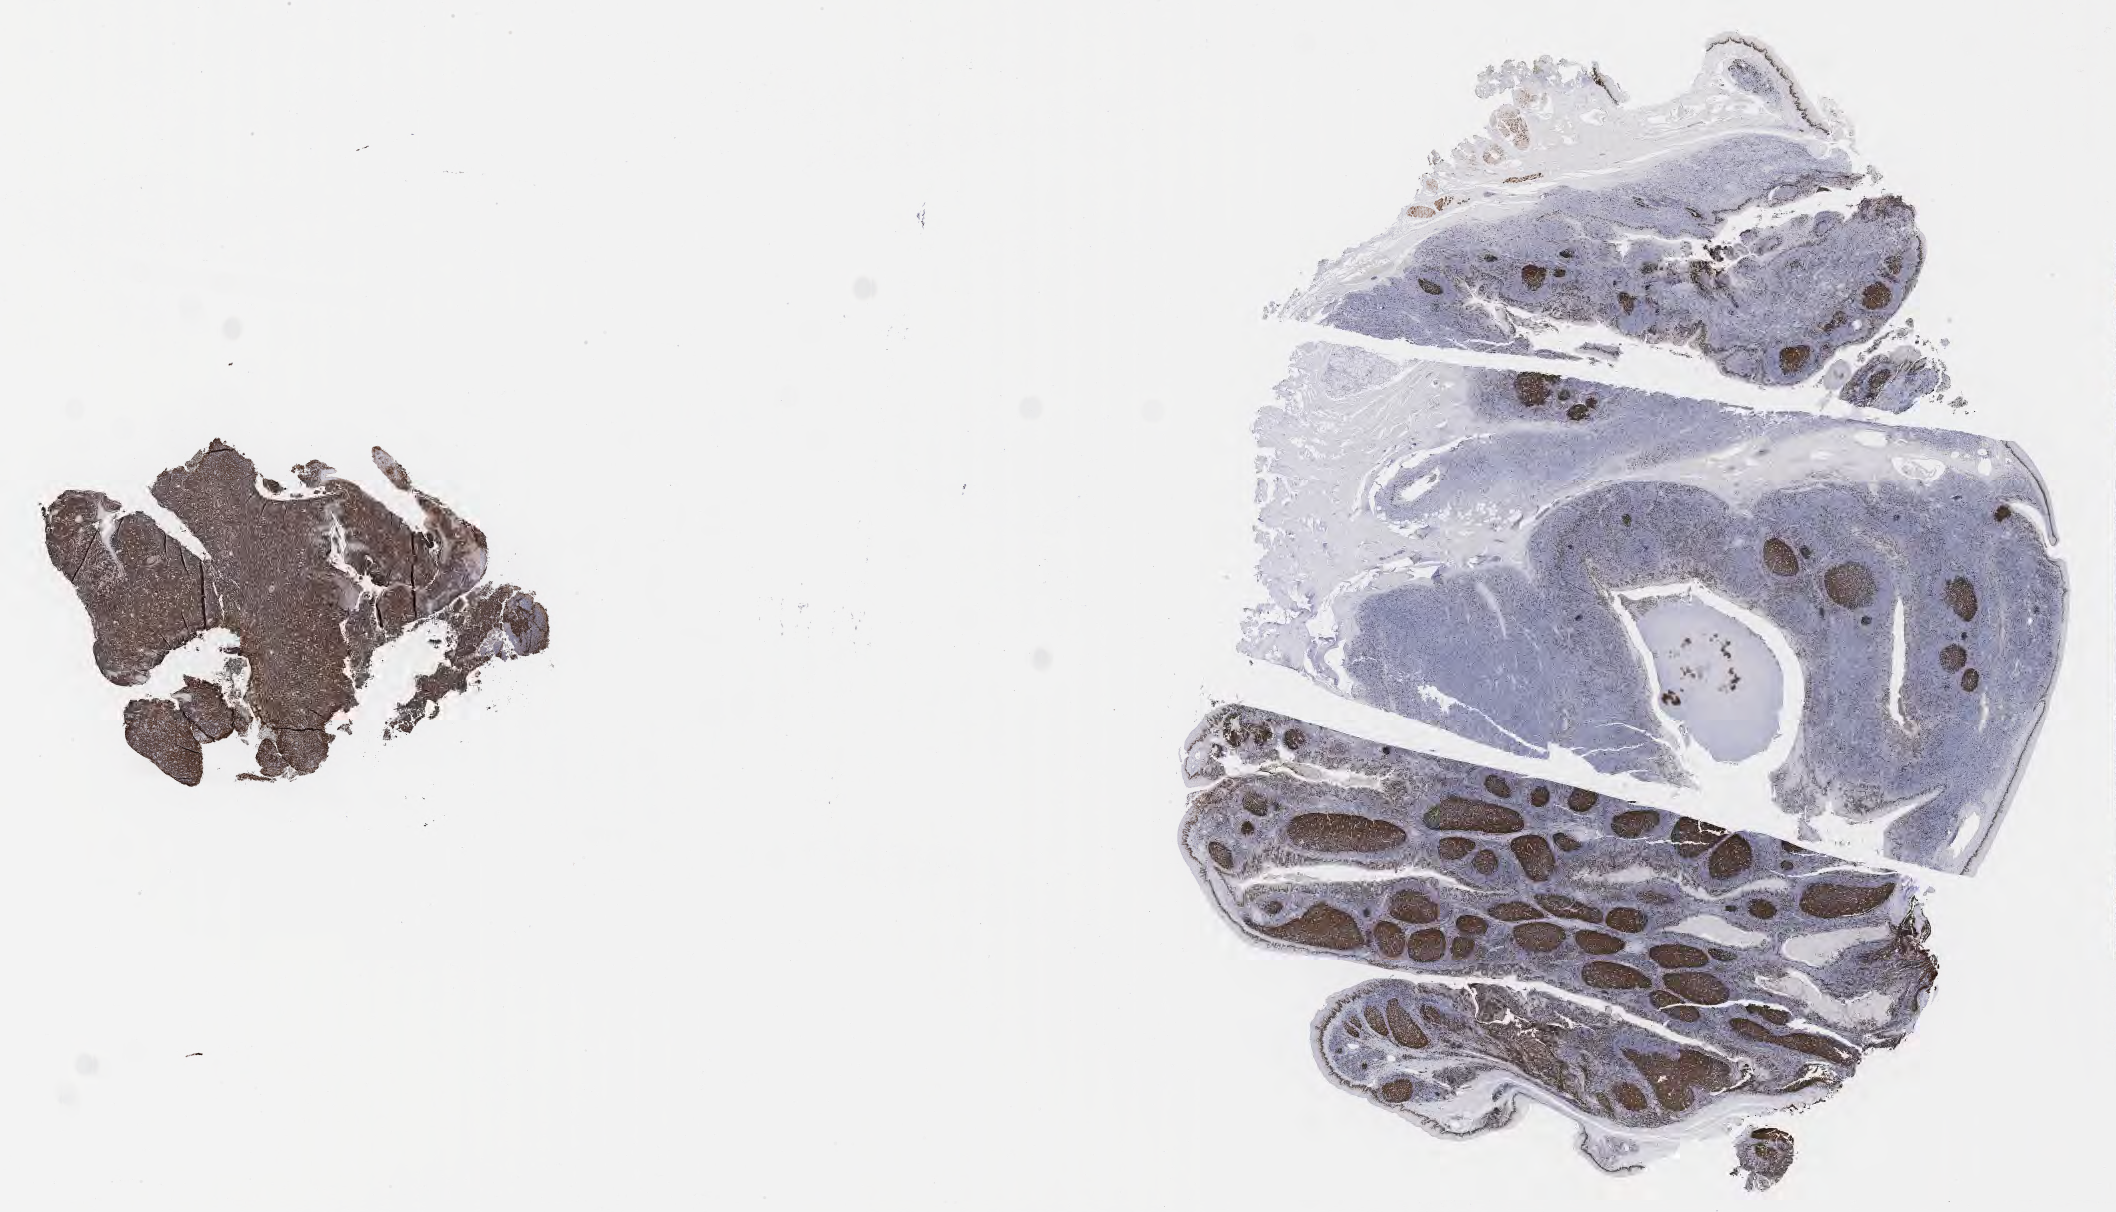
IHC for Ki-67, whole-slide image — whole scanned area (about 34.2 x 19.6 mm) shown as a low-resolution overview. Tumor tissue. Male patient; age at initial diagnosis 3 years.
Diagnosis: Burkitt lymphoma, NOS.